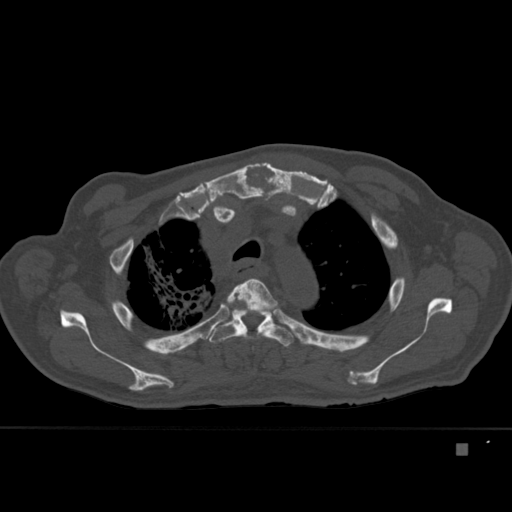
CT including the spine, one axial slice; slice 327 of 451 in the series (ordered by position); bone window (W 1800 / L 400 HU); 512 × 512 image matrix. Male patient, age 75 years. Case-level facts recorded for this patient, not image findings: primary cancer: prostate.
Structures marked on this image (semi-automatically segmented with operator editing):
- T3 vertebra: bounding box [x1, y1, x2, y2] px = [223, 278, 278, 348]
- T4 vertebra: [207, 308, 293, 347]